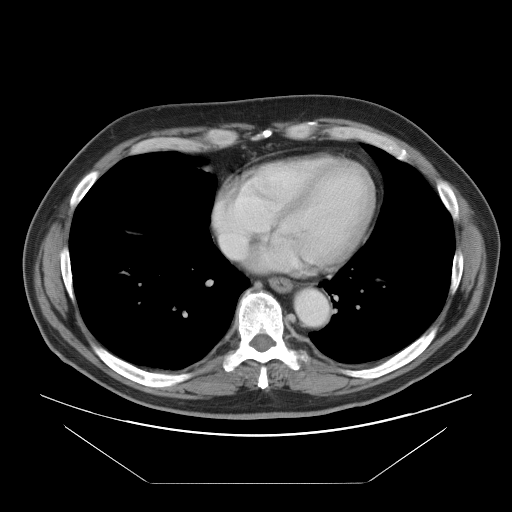
Contrast-enhanced abdominal CT, one axial slice; slice 94 of 97 in the series (ordered by position); intravenous contrast given; soft-tissue window (W 400 / L 40 HU); 512 × 512 image matrix, field of view 442 × 442 mm. Male patient, age 62 years. From the clinical record (not read from this slice): diagnosis: colorectal cancer liver metastases, imaged before liver resection; multiple liver metastases: no; largest metastasis: 7 cm; chemotherapy before resection: yes.
Outlined on this slice (manually delineated by an expert):
- hepatic veins: bounding box <214,184,247,260> (left, top, right, bottom; pixels)